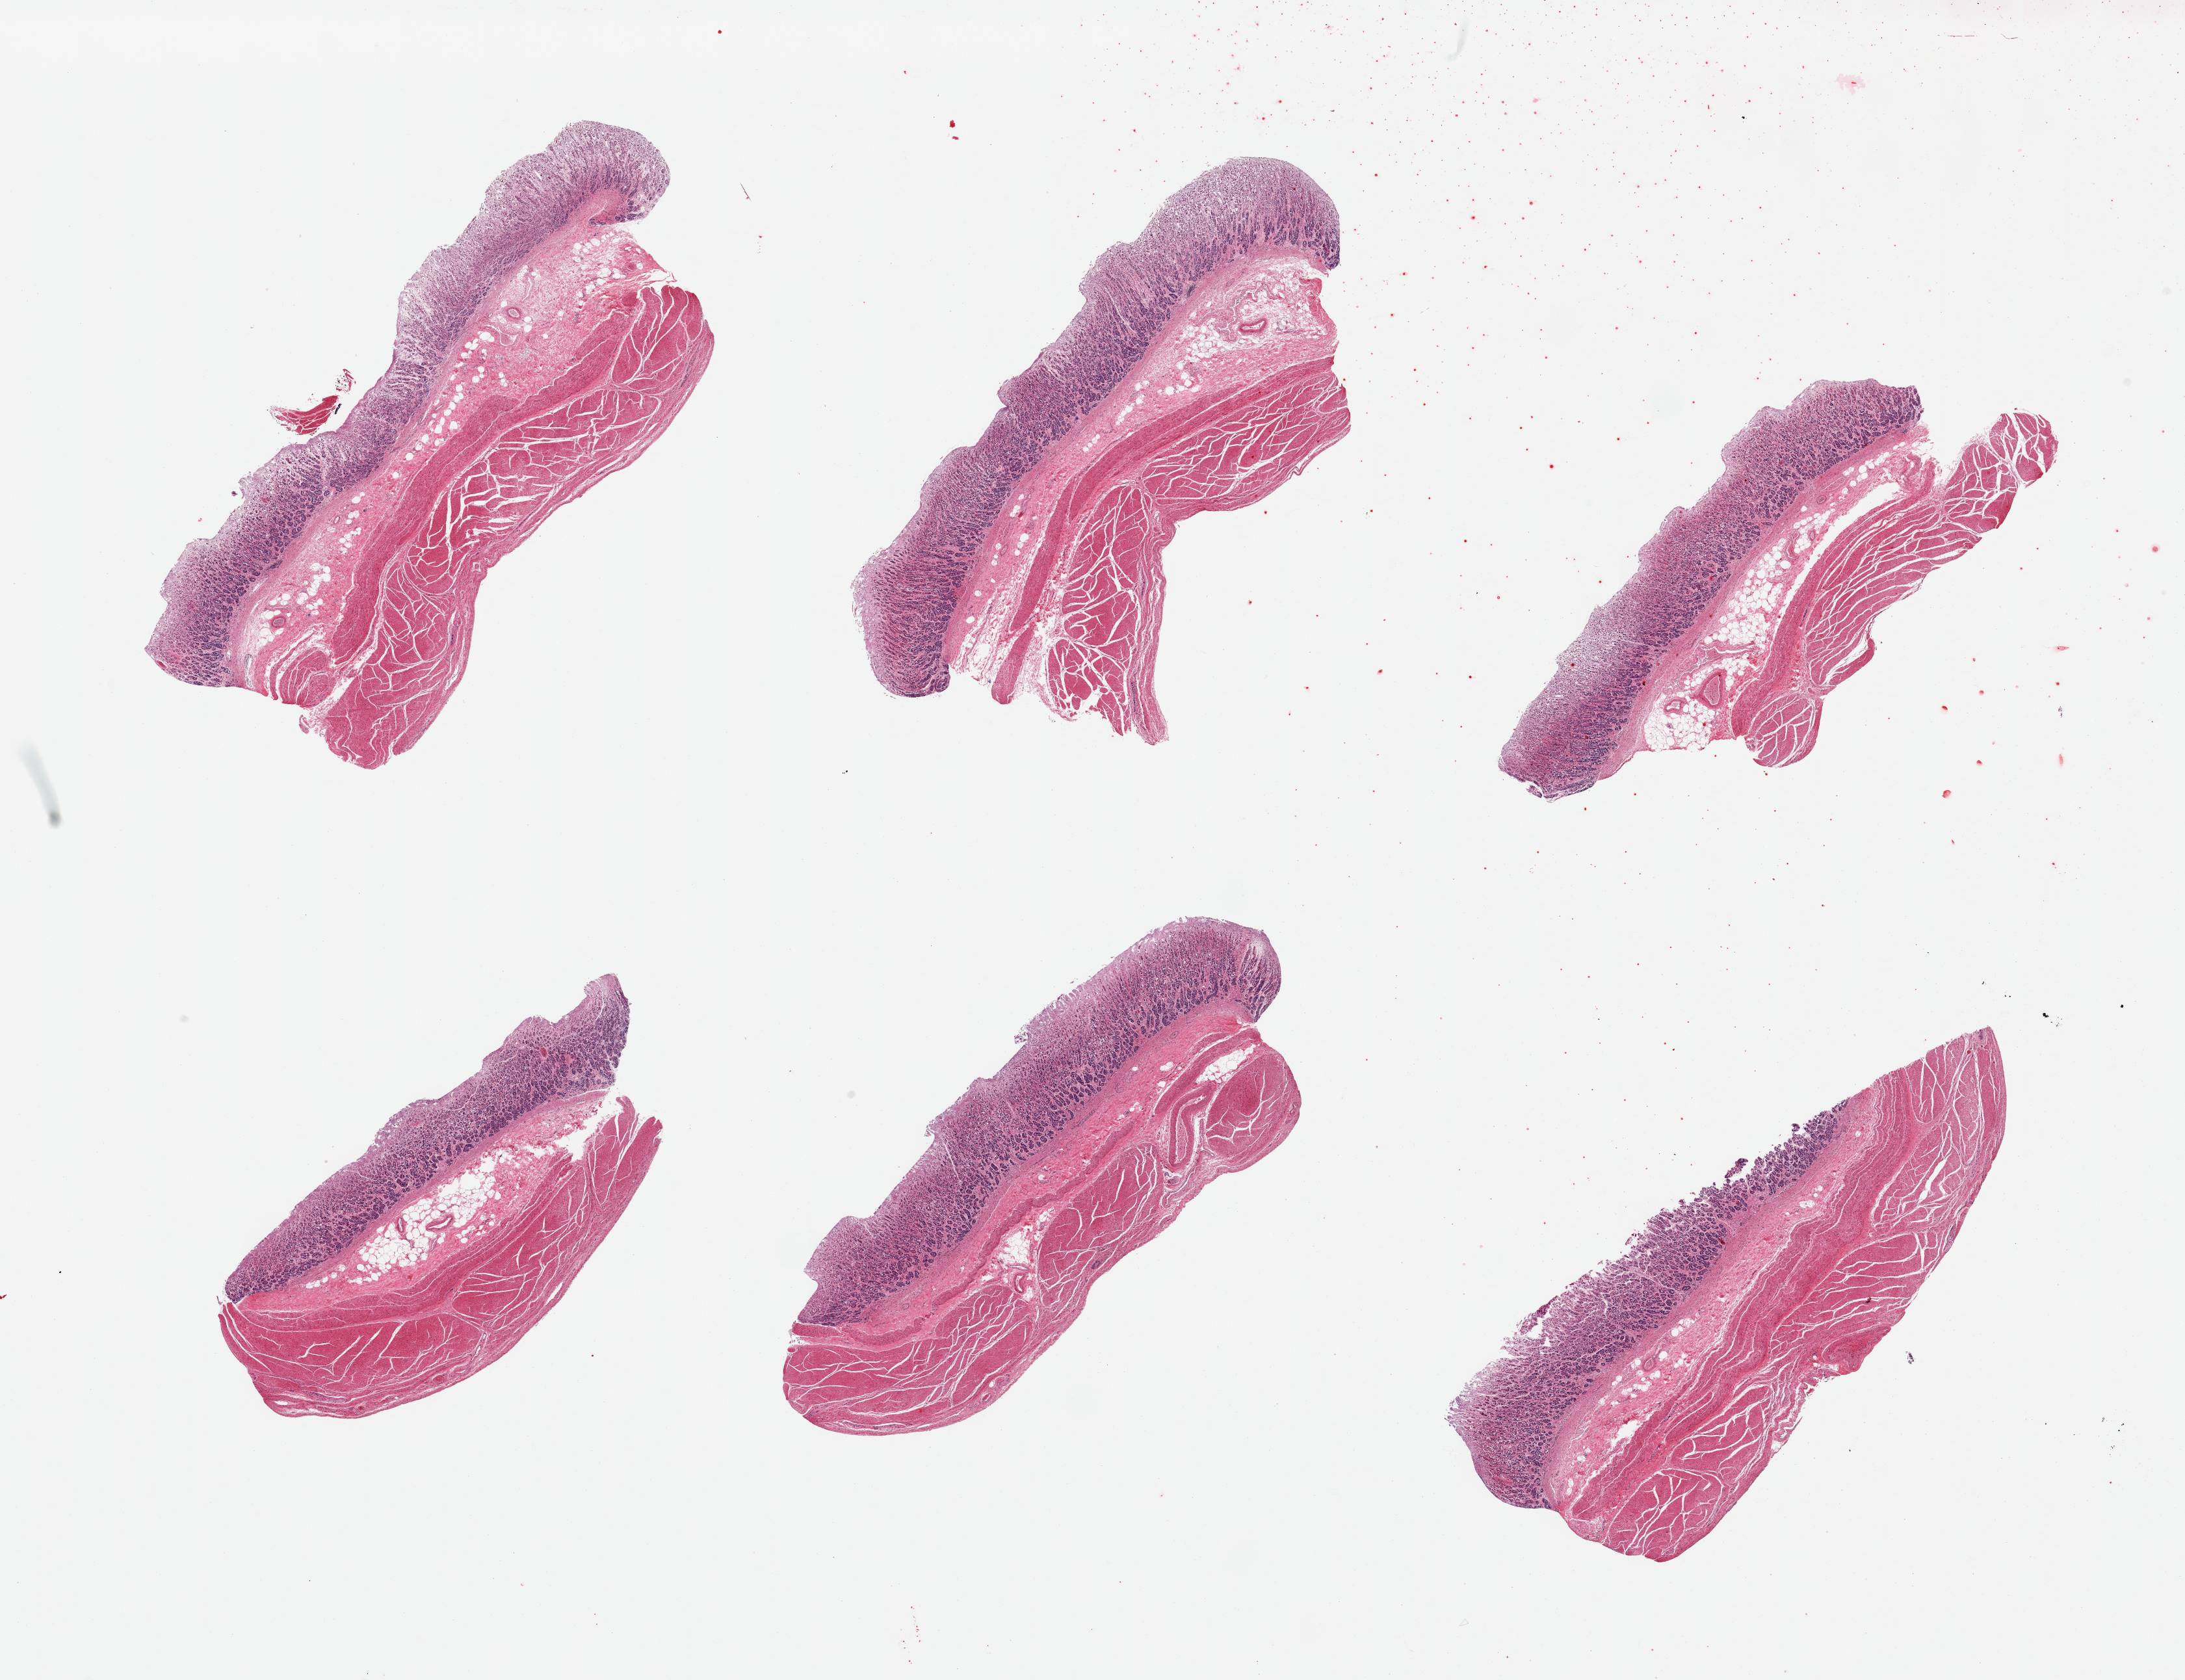
Whole-slide image, haematoxylin and eosin stain, whole scanned area (about 26.6 x 20.4 mm) shown as a low-resolution overview; PAXgene-fixed paraffin-embedded (PFPE) section; sampled site (target tissue): stomach; tissue donor sample. Donor: male.
• pathologist's review note for this sample: 6 pieces, mucosa up to ~1mm, ~30% thickness, moderately advanced autolysis